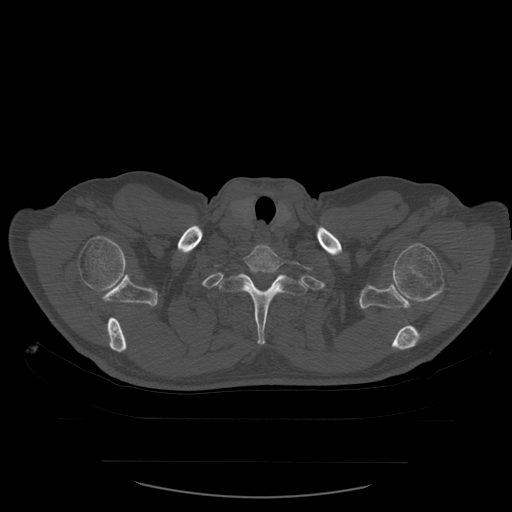
CT including the spine, one axial slice. Position 479 of 590 along the scan axis. Bone window (W 1800 / L 400 HU). 512 × 512 image matrix, field of view 479 × 479 mm. Patient age 71 years. Case-level facts recorded for this patient, not image findings: primary cancer: lung.
Outlined on this slice (semi-automatically segmented with operator editing):
- T1 vertebra: bounding box <245,246,311,289> (left, top, right, bottom; pixels)
- T2 vertebra: <218,274,309,345>
- T3 vertebra: <224,302,227,304>